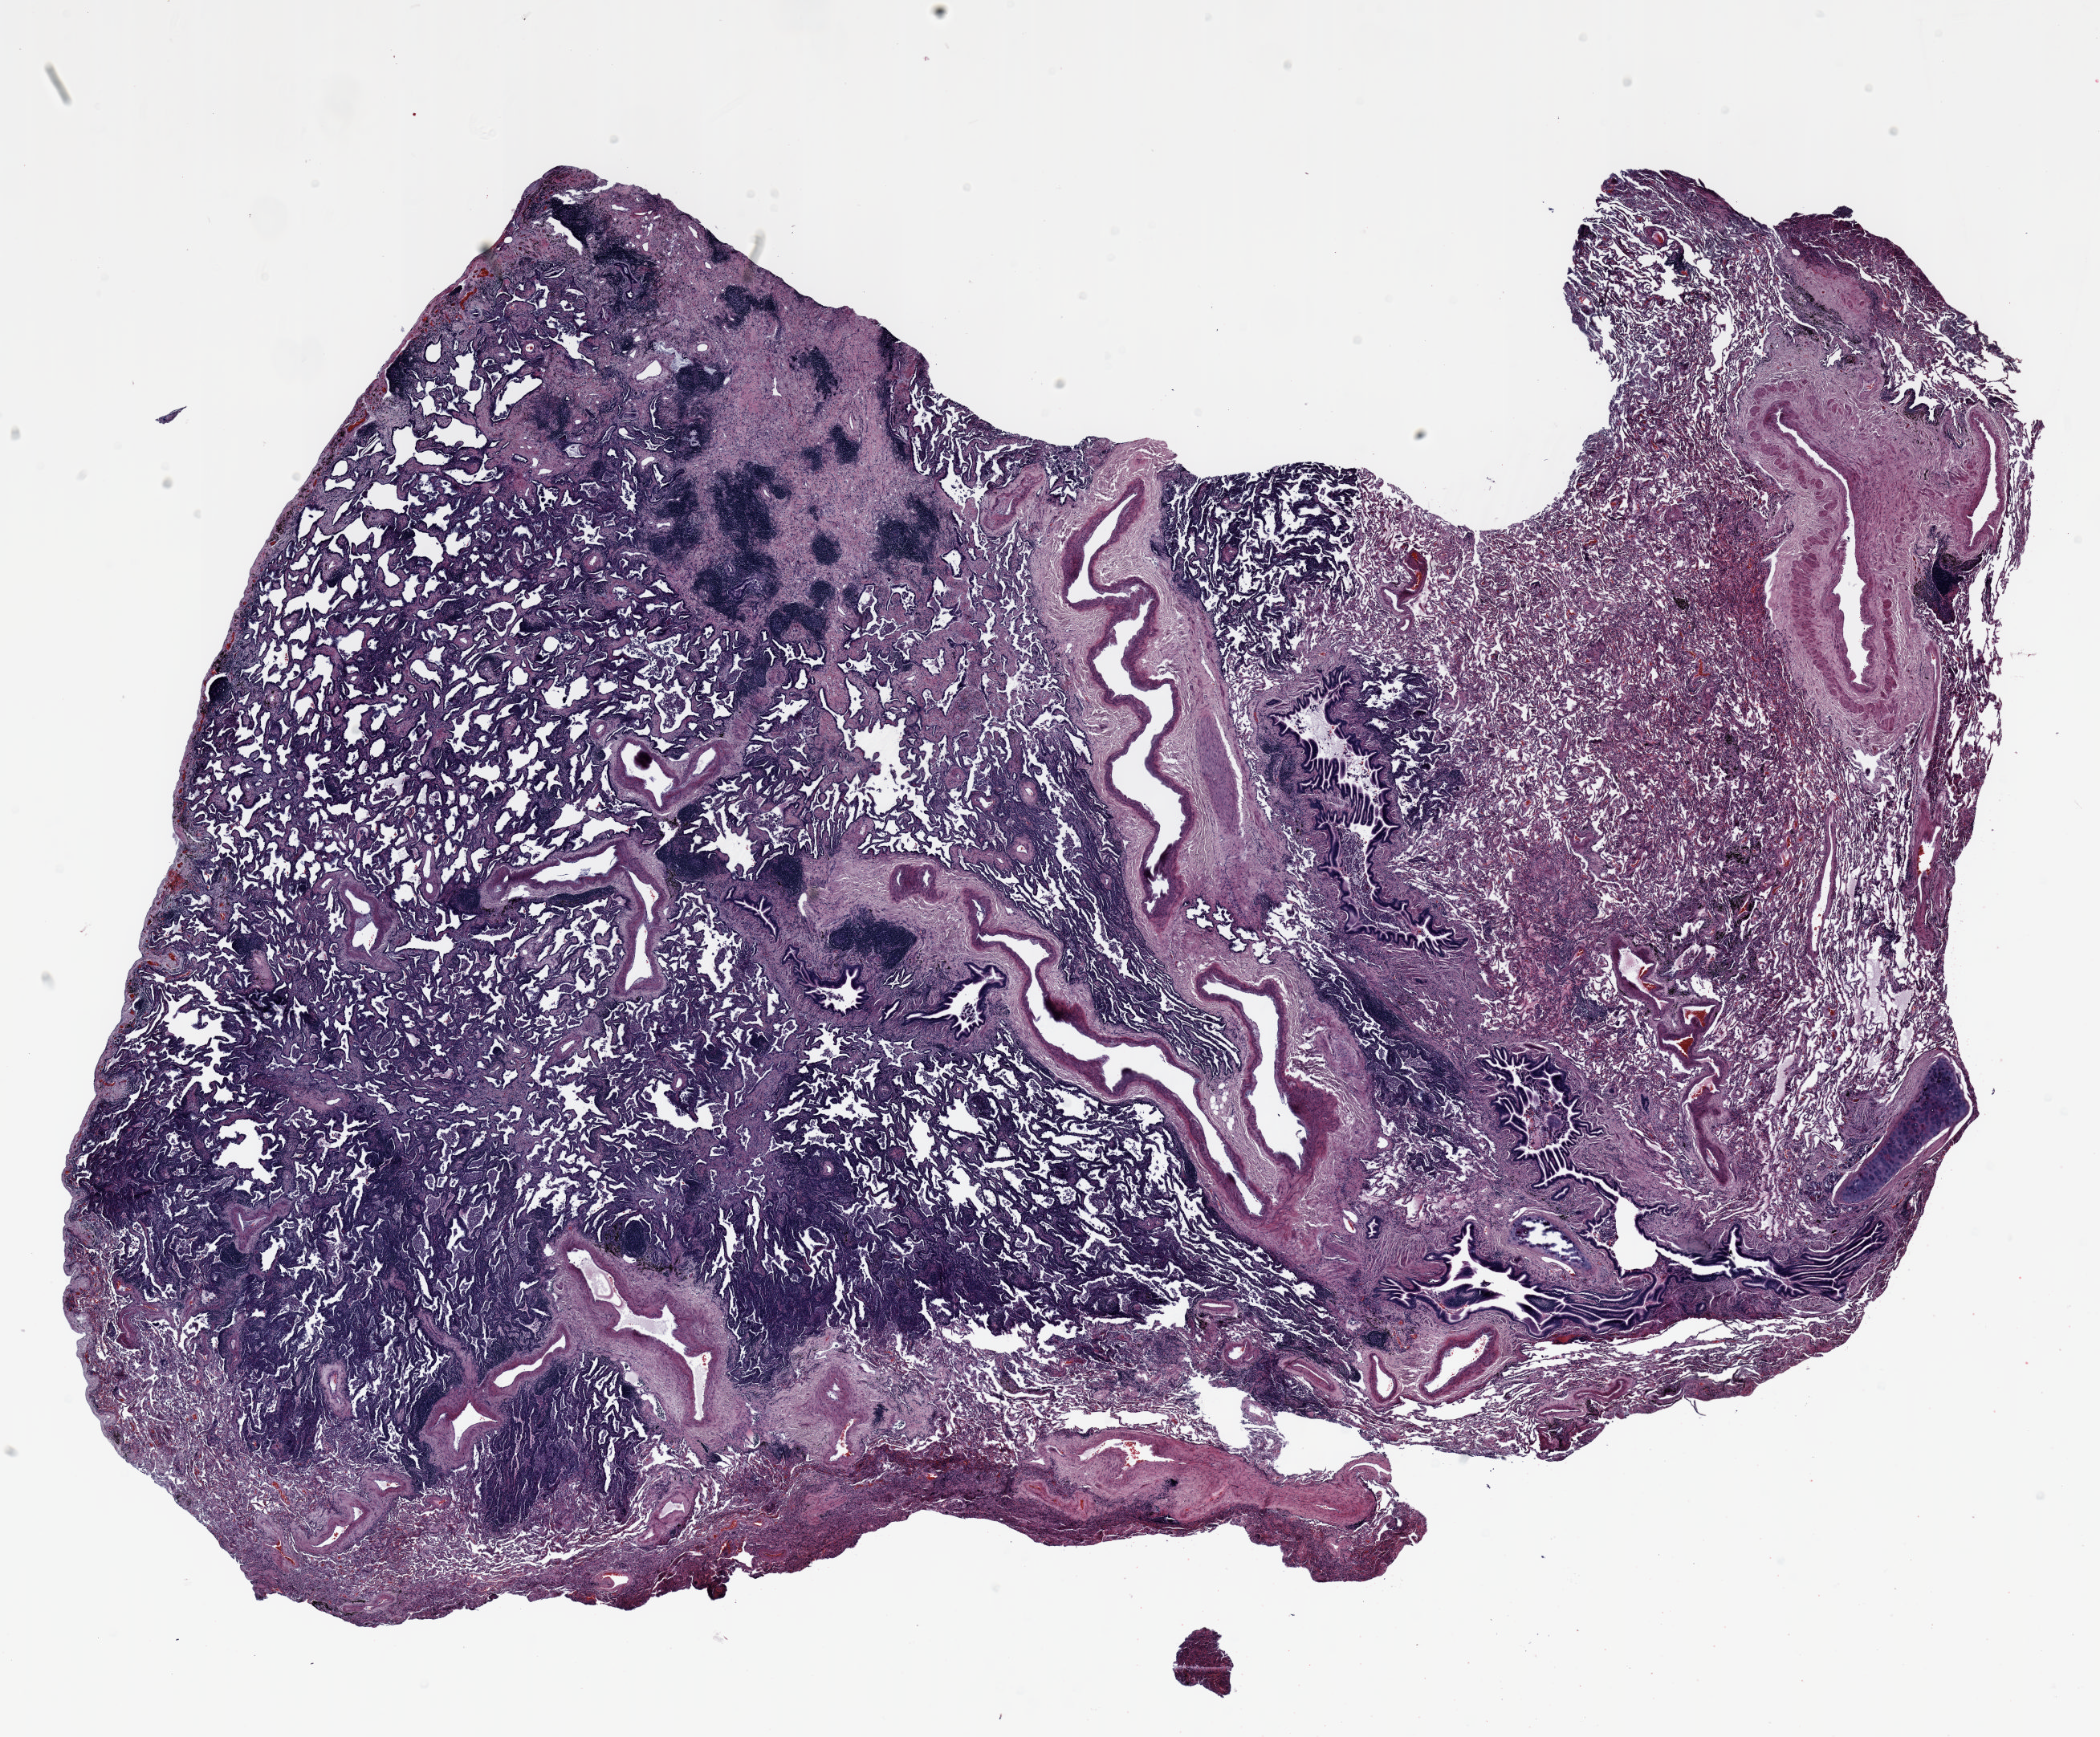
Whole-slide histology image, H&E — whole scanned area (about 21.0 x 17.4 mm, acquisition: 20x scan) shown as a low-resolution overview, formalin-fixed paraffin-embedded (FFPE) section, lung tissue. Male, age 69 at enrolment. Grade: well differentiated (G1).
ICD-O-3 topography: lower lobe of lung (C34.3). Tumour size (pathology): 23 mm. Primary tumour location (clinical record): right lower lobe. Participant's lung-cancer diagnosis: Bronchiolo-alveolar adenocarcinoma, NOS (ICD-O-3 8250/3). Stage (AJCC 6th edition): IB.